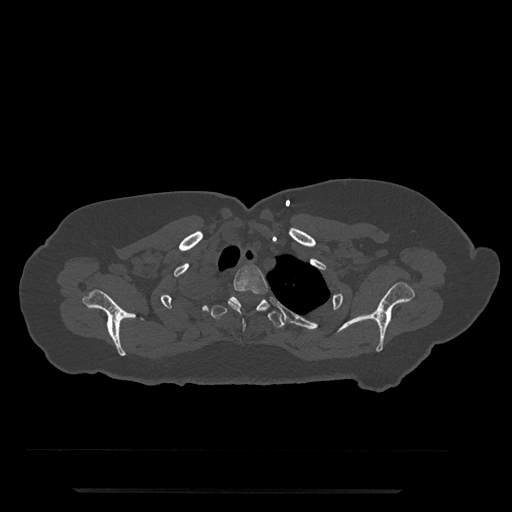
CT including the spine, one axial slice. Slice 657 of 797 in the series (ordered by position). Reconstruction kernel Br40s/3. 120 kVp. Bone window (W 1800 / L 400 HU). 0.5 mm slice thickness. 512 × 512 image matrix, field of view 440 × 440 mm. Female patient, age 51 years. Case-level facts recorded for this patient, not image findings: primary cancer: neuro; vertebrae with lytic lesions (as recorded): T8.
Structures marked on this image (semi-automatic segmentation, software-assisted and operator-edited):
- T2 vertebra: bounding box <228,265,268,330> (left, top, right, bottom; pixels)
- T3 vertebra: <211,296,284,328>